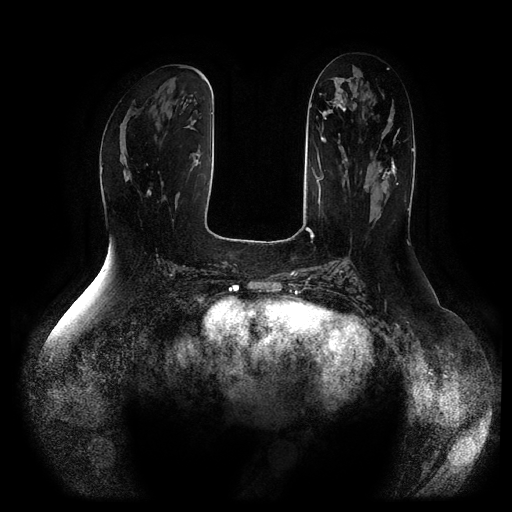
Breast MRI (dynamic contrast-enhanced, multi-phase), one axial slice. Position 40 of 116 along the scan axis. Dynamic contrast-enhanced series, time point 2 of 5 at this slice position (early post-contrast). 1.5 T. TE 2.5 ms, TR 5.2 ms. 512 × 512 image matrix, field of view 400 × 400 mm. Female patient, age 66 years.
Annotated regions visible in this slice (semi-automatically segmented with operator editing):
- breast lesion (labelled 'tumour' in the annotation; benign lesions carry a separate 'benign' label): bounding box (x1, y1, x2, y2) in pixels: (379, 161, 397, 179)